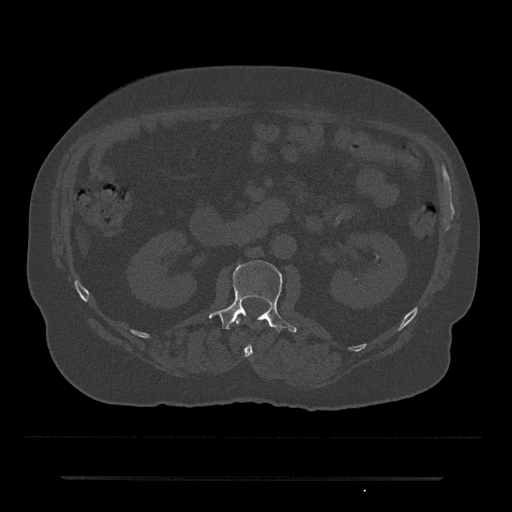
CT including the spine, one axial slice. Slice 23 of 797 in the series (ordered by position). 120 kVp. Bone window (W 1800 / L 400 HU). 0.5 mm slice thickness. 512 × 512 image matrix. Male patient, age 69 years. From the clinical record (not read from this slice): primary cancer: prostate.
Annotated regions visible in this slice (semi-automatic segmentation, software-assisted and operator-edited):
- L1 vertebra: bounding box <235,317,253,357> (left, top, right, bottom; pixels)
- L2 vertebra: <209,260,297,333>